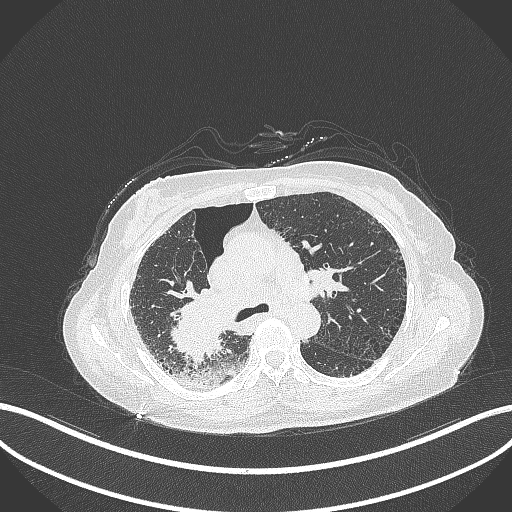
Chest CT, one axial slice; position 223 of 408 along the scan axis; reconstruction kernel B70f; lung window (W 1500 / L -600 HU); 512 × 512 image matrix, field of view 400 × 400 mm. Patient: female, 64 years. Case-level facts recorded for this patient, not image findings: clinical TNM (as recorded): T3 N3 M0.
Outlined on this slice (bounding box drawn by a radiologist):
- lung tumour (recorded histology: squamous cell carcinoma): bounding box (x1, y1, x2, y2) in pixels: (167, 282, 232, 364)